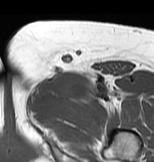
MRI of an extremity soft-tissue mass, one axial slice. Position 46 of 83 along the scan axis. MR volume resampled by the dataset authors to the PET/CT grid (not the native acquisition matrix). 3.27 mm slice thickness. 154 × 162 image matrix, field of view 150 × 158 mm. Female patient. Case-level facts recorded for this patient, not image findings: histological type: myxofibrosarcoma; grade: intermediate; site of the primary tumour: left thigh.
Outlined on this slice (expert contour drawn on MRI and transferred to this co-registered scan by the dataset authors):
- gross tumour volume including surrounding oedema: box from (x=26, y=70) to (x=127, y=115) px
- gross tumour volume (mass): (x=62, y=71)–(x=84, y=90)